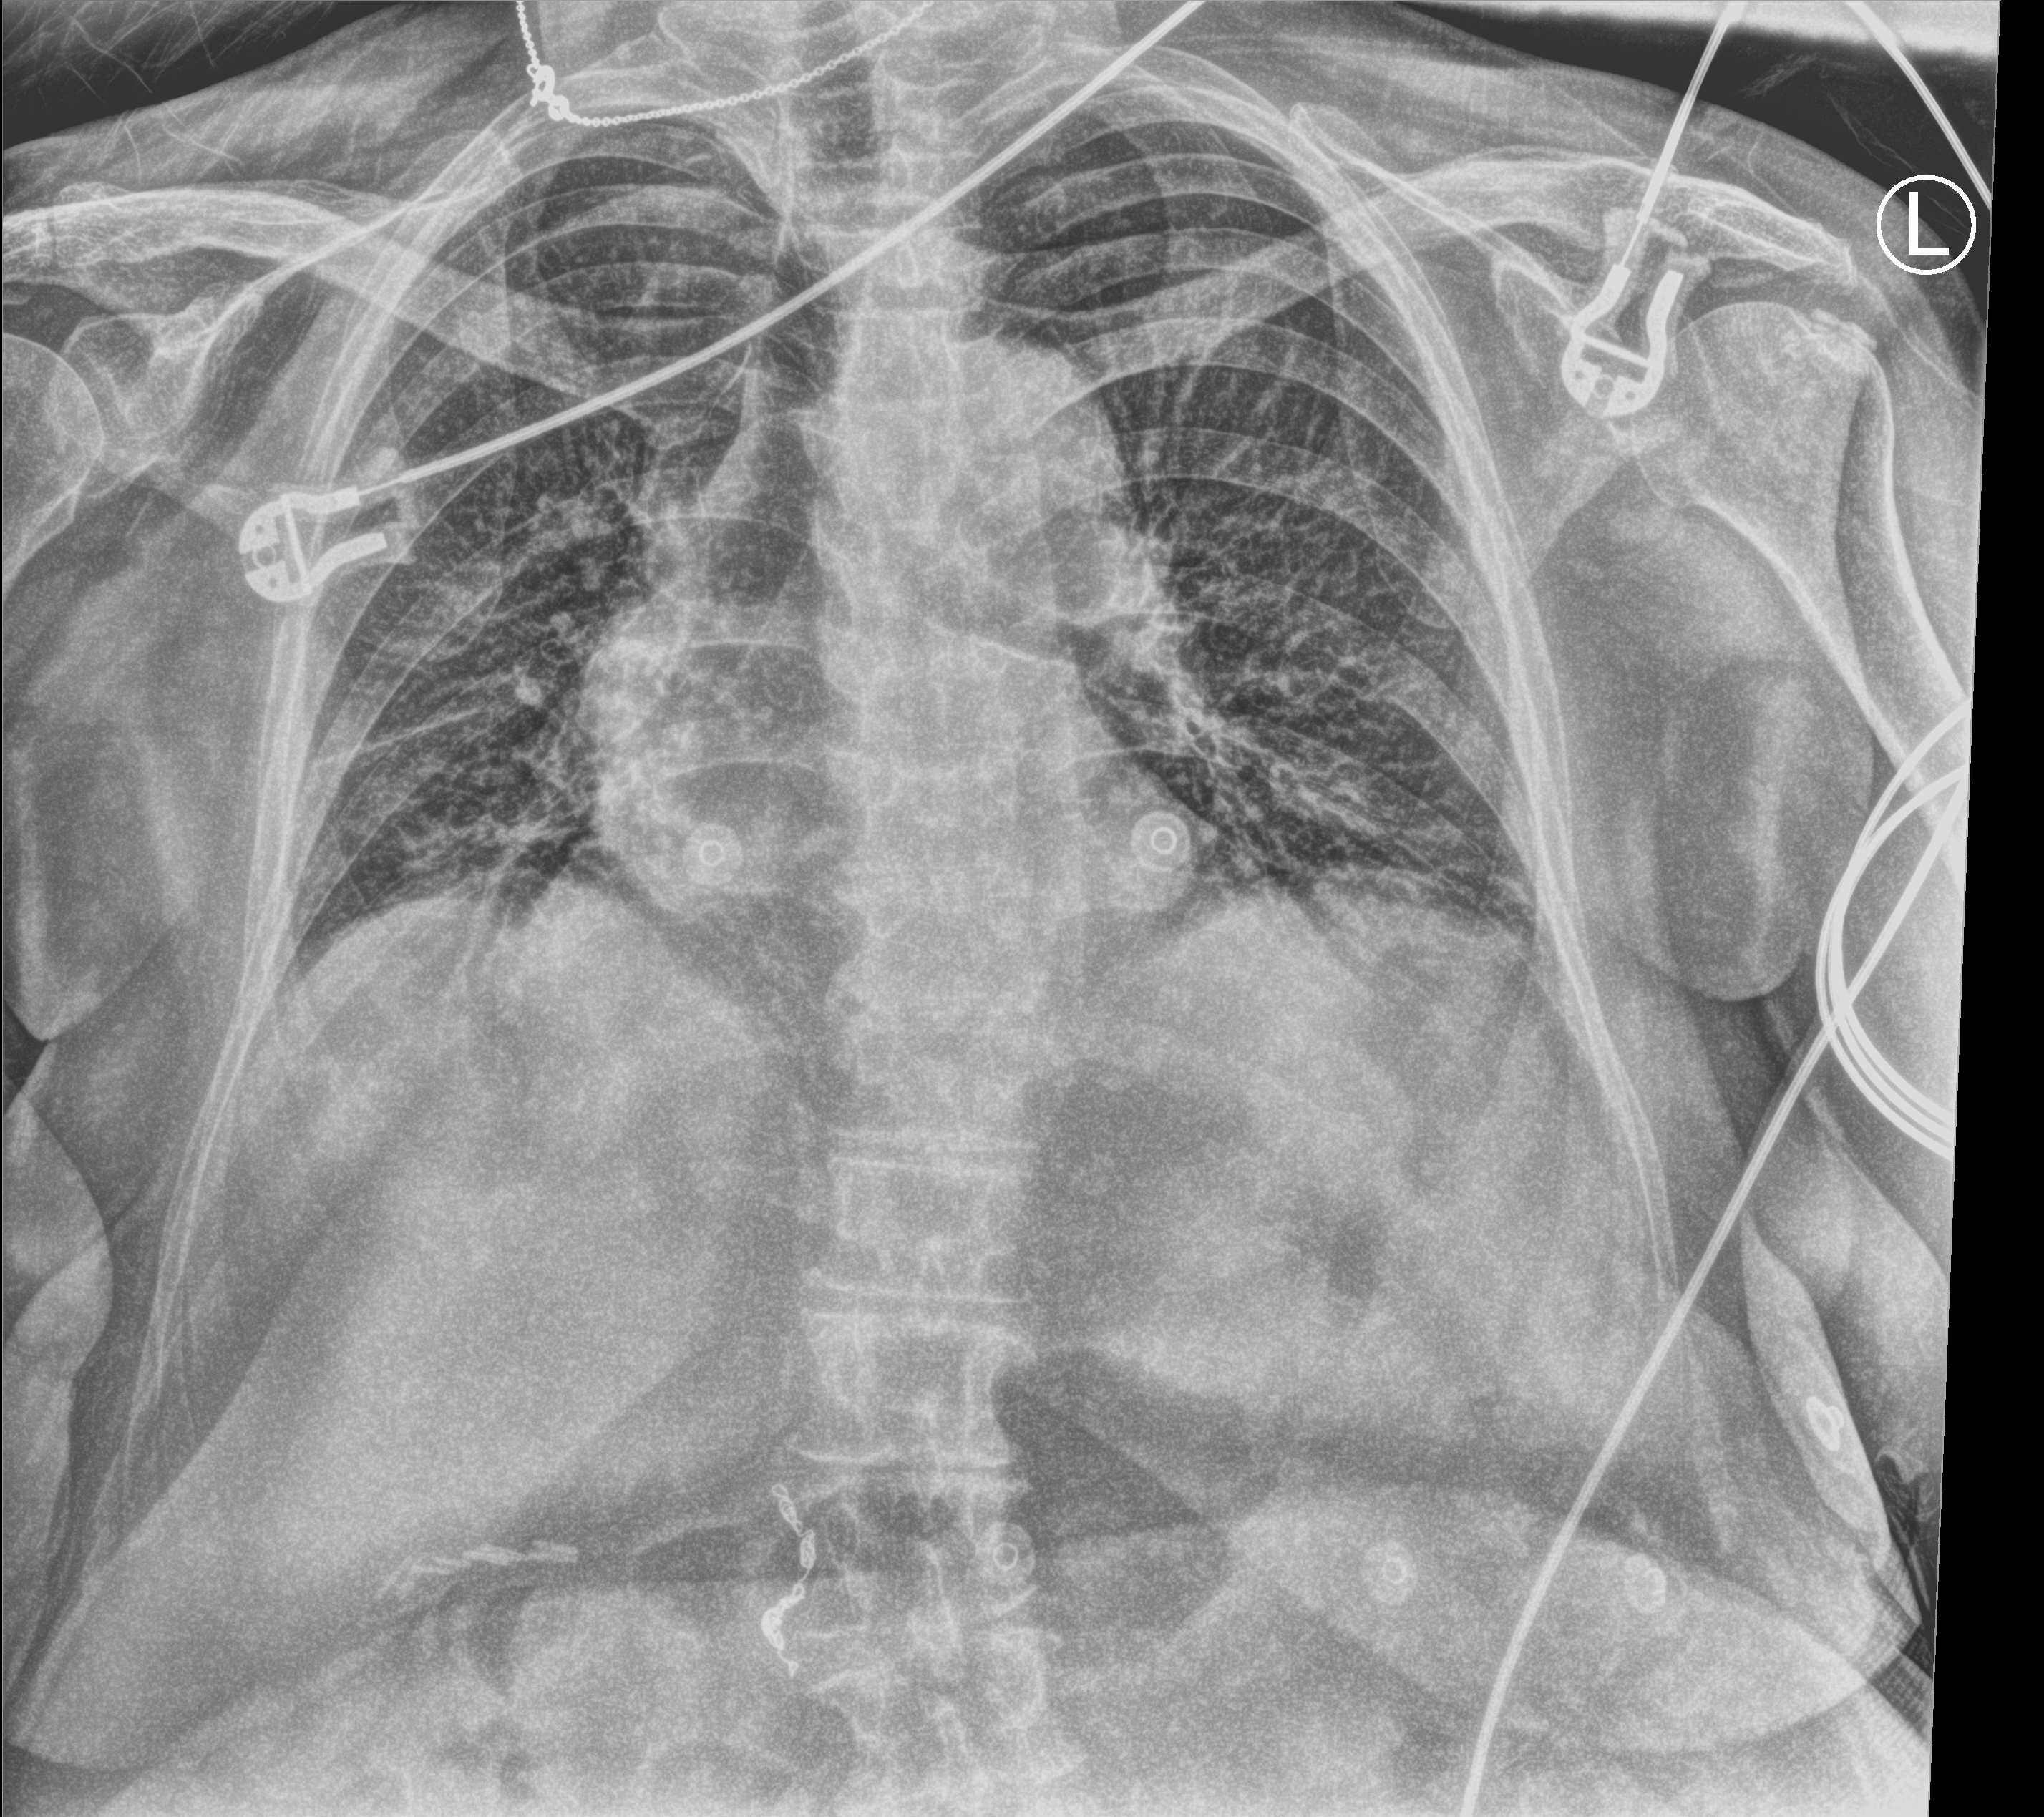
Chest X-ray (portable). Patient hospitalised with COVID-19; female, aged 75–90 years.
Admission-level facts for this patient (not findings on this image; timing relative to this image not recorded): admitted to intensive care during this hospital stay: no.